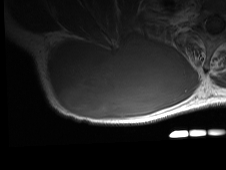
MRI of an extremity soft-tissue mass, one axial slice; slice 44 of 81 in the series (ordered by position); MR volume resampled by the dataset authors to the PET/CT grid (not the native acquisition matrix); 3.27 mm slice thickness; 226 × 170 image matrix. Male patient. Case-level facts recorded for this patient, not image findings: histological type: pleiomorphic spindle cell undifferentiated; grade: high; site of the primary tumour: right parascapusular.
Outlined on this slice (expert contour drawn on MRI and transferred to this co-registered scan by the dataset authors):
- gross tumour volume including surrounding oedema: bounding box (x1, y1, x2, y2) in pixels: (46, 33, 200, 121)
- gross tumour volume (mass): (46, 36, 186, 117)